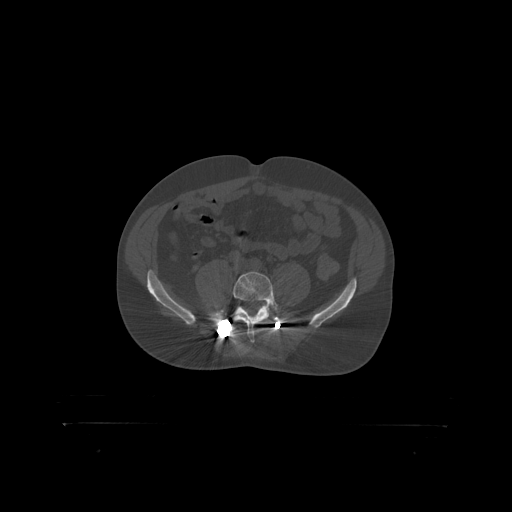
CT including the spine, one axial slice; position 205 of 399 along the scan axis; reconstruction kernel STANDARD; 120 kVp; bone window (W 1800 / L 400 HU); 1.25 mm slice thickness; 512 × 512 image matrix, field of view 650 × 650 mm. Patient: male, 46 years. From the clinical record (not read from this slice): primary cancer: skin.
Outlined on this slice (semi-automatic segmentation, software-assisted and operator-edited):
- L5 vertebra: bounding box (x1, y1, x2, y2) in pixels: (233, 272, 279, 319)